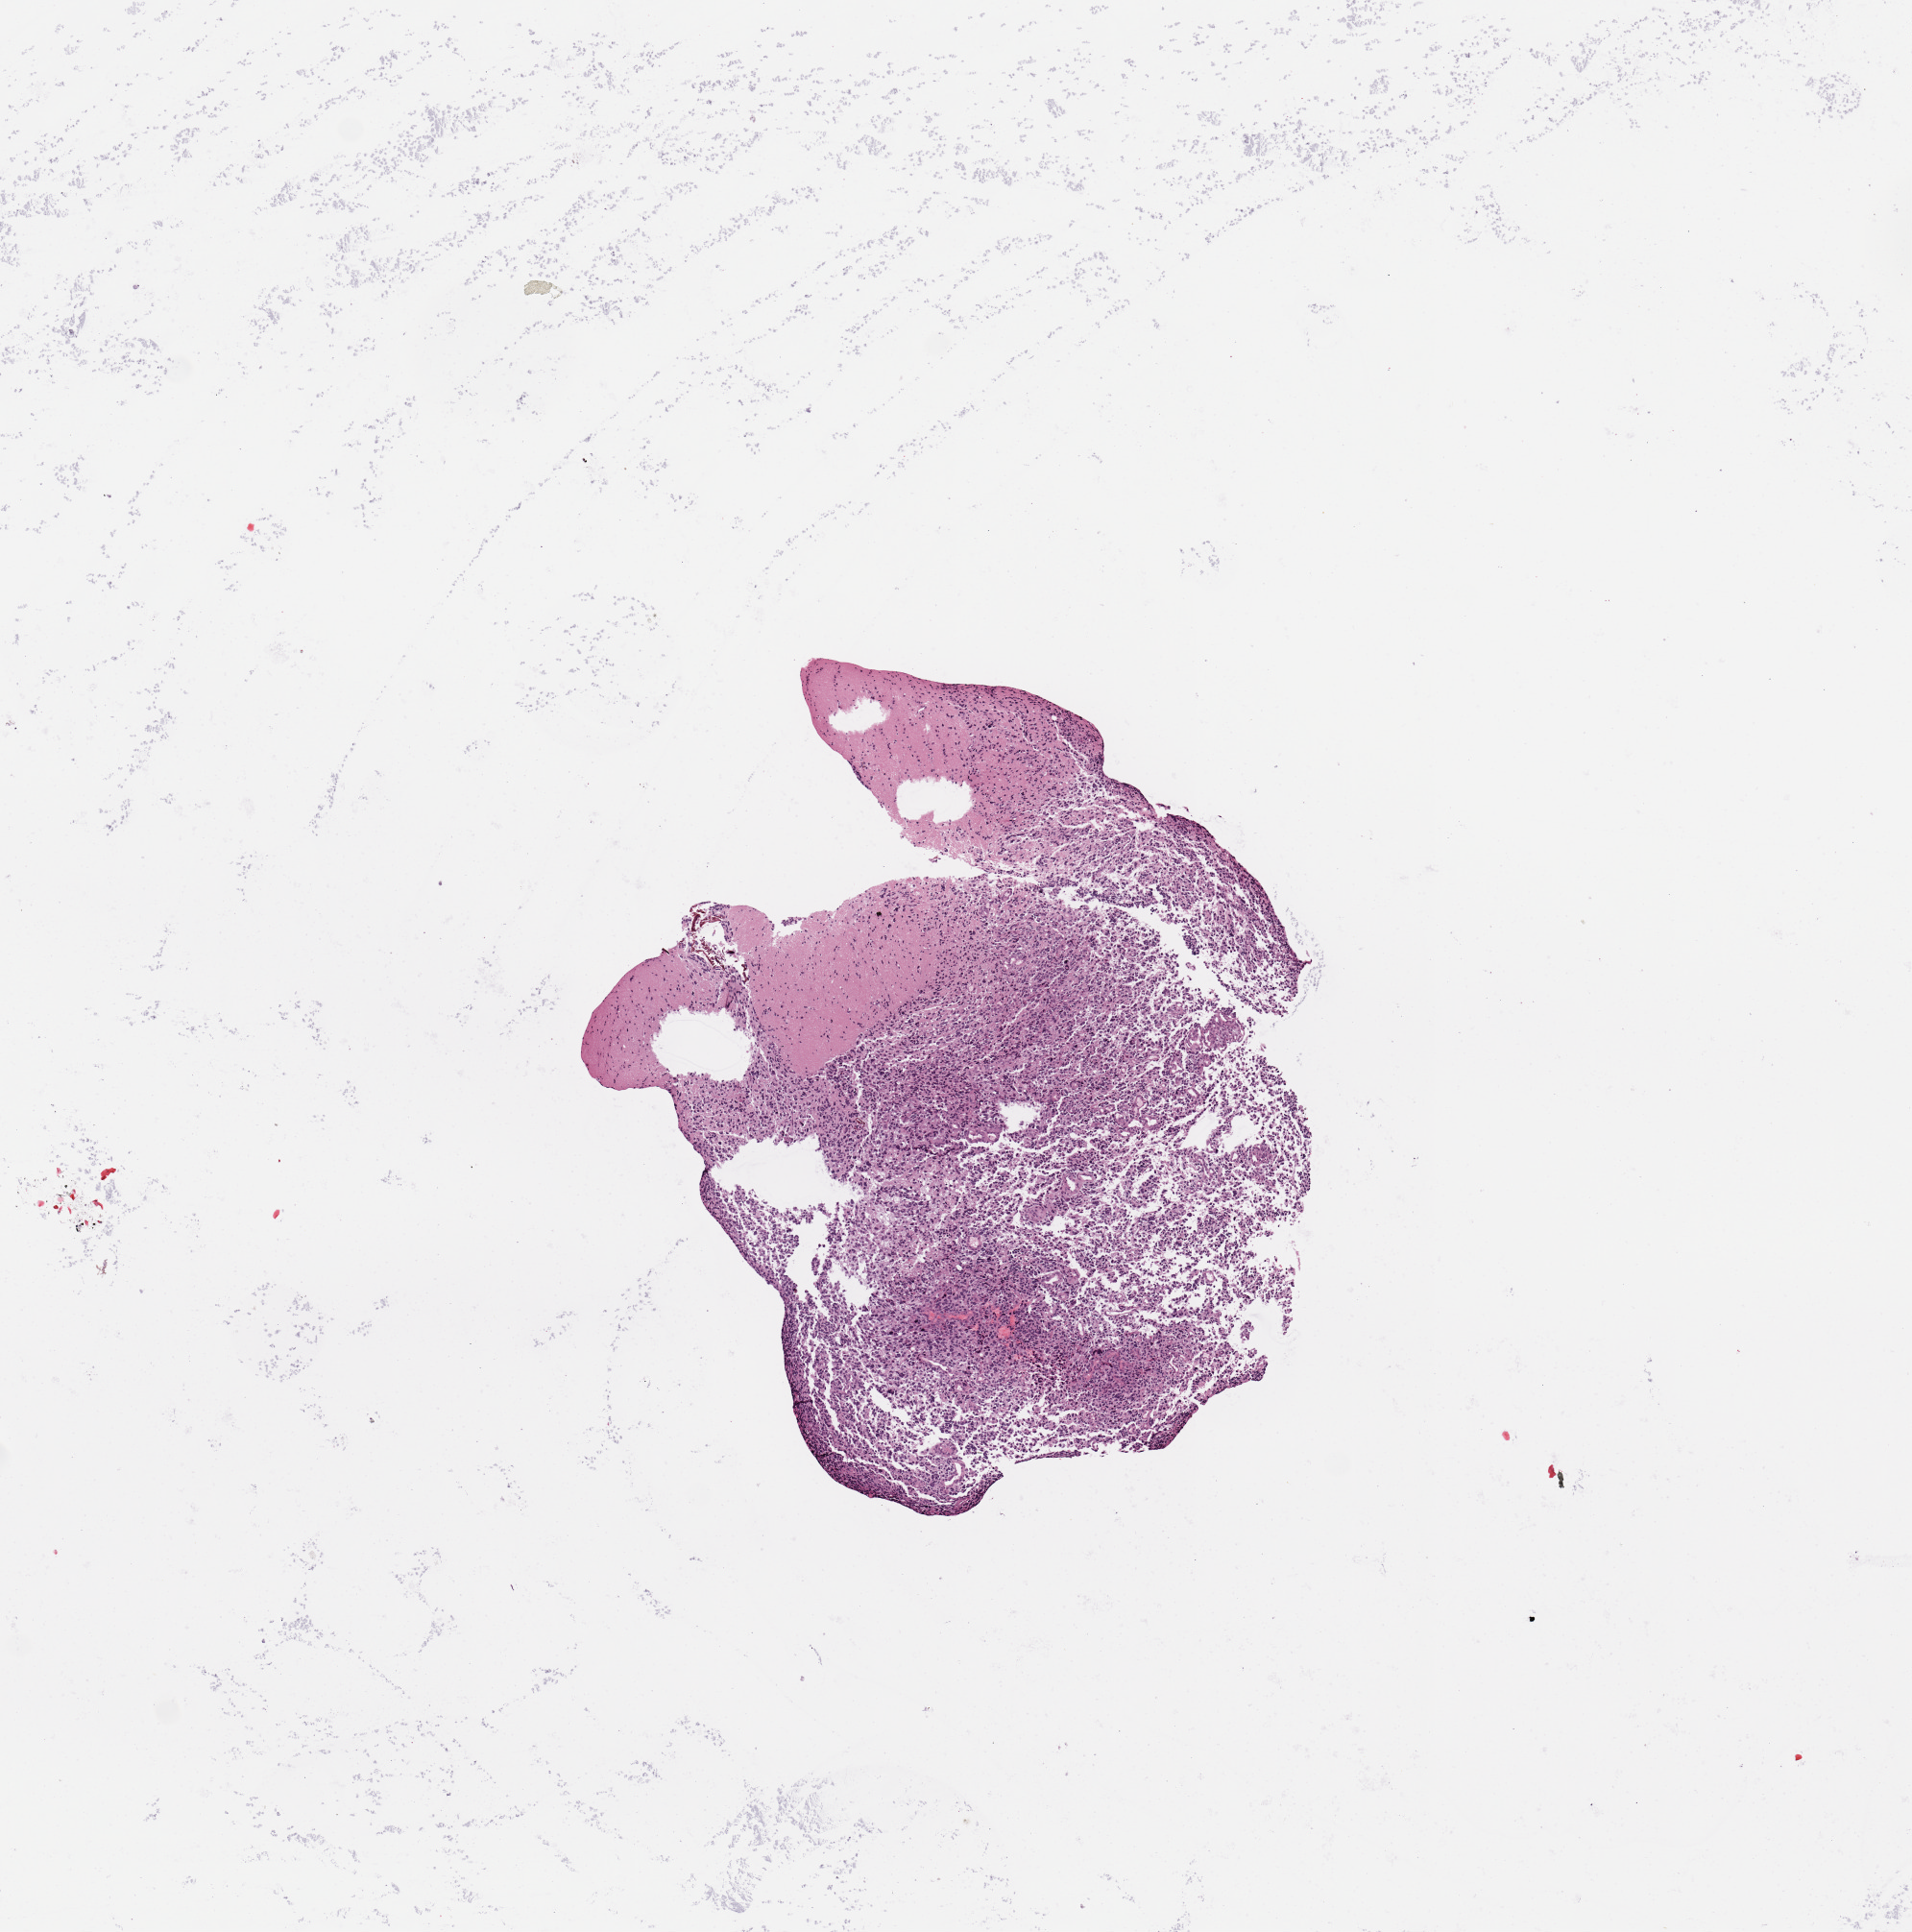
Whole-slide histology image, Hematoxylin and eosin (H&E) stained, whole scanned area (about 7.9 x 8.0 mm, from a 20x scan) shown as a low-resolution overview; tumour tissue sample, brain. Female, 30 y/o.
• diagnosis: Glioblastoma